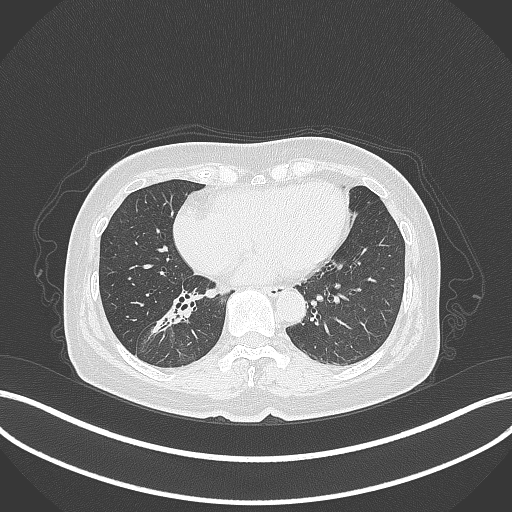
Chest CT, one axial slice; slice 151 of 429 in the series (ordered by position); reconstruction kernel B70f; 120 kVp; lung window (W 1500 / L -600 HU); 1 mm slice thickness; 512 × 512 image matrix, field of view 400 × 400 mm. Patient: female, 67 years. From the clinical record (not read from this slice): clinical TNM (as recorded): T1c N1 M0.
Outlined on this slice (rectangle marked by the reading radiologist):
- lung tumour (recorded histology: adenocarcinoma): bounding box <143,295,198,336> (left, top, right, bottom; pixels)